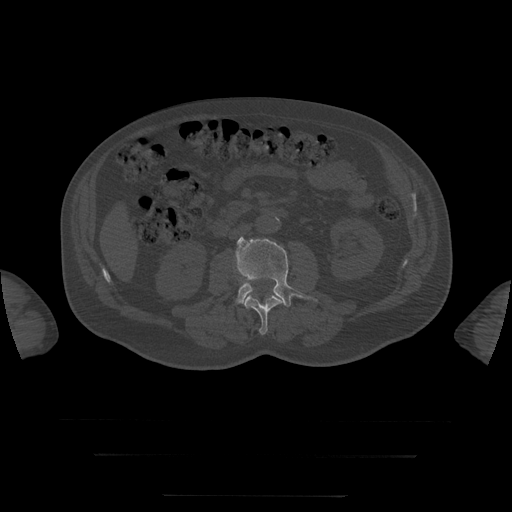
CT including the spine, one axial slice; slice 8 of 397 in the series (ordered by position); reconstruction kernel STANDARD; bone window (W 1800 / L 400 HU); 1.25 mm slice thickness; 512 × 512 image matrix. Patient age 73 years. From the clinical record (not read from this slice): primary cancer: prostate.
Outlined on this slice (semi-automatically segmented with operator editing):
- L3 vertebra: box from (x=236, y=237) to (x=318, y=308) px